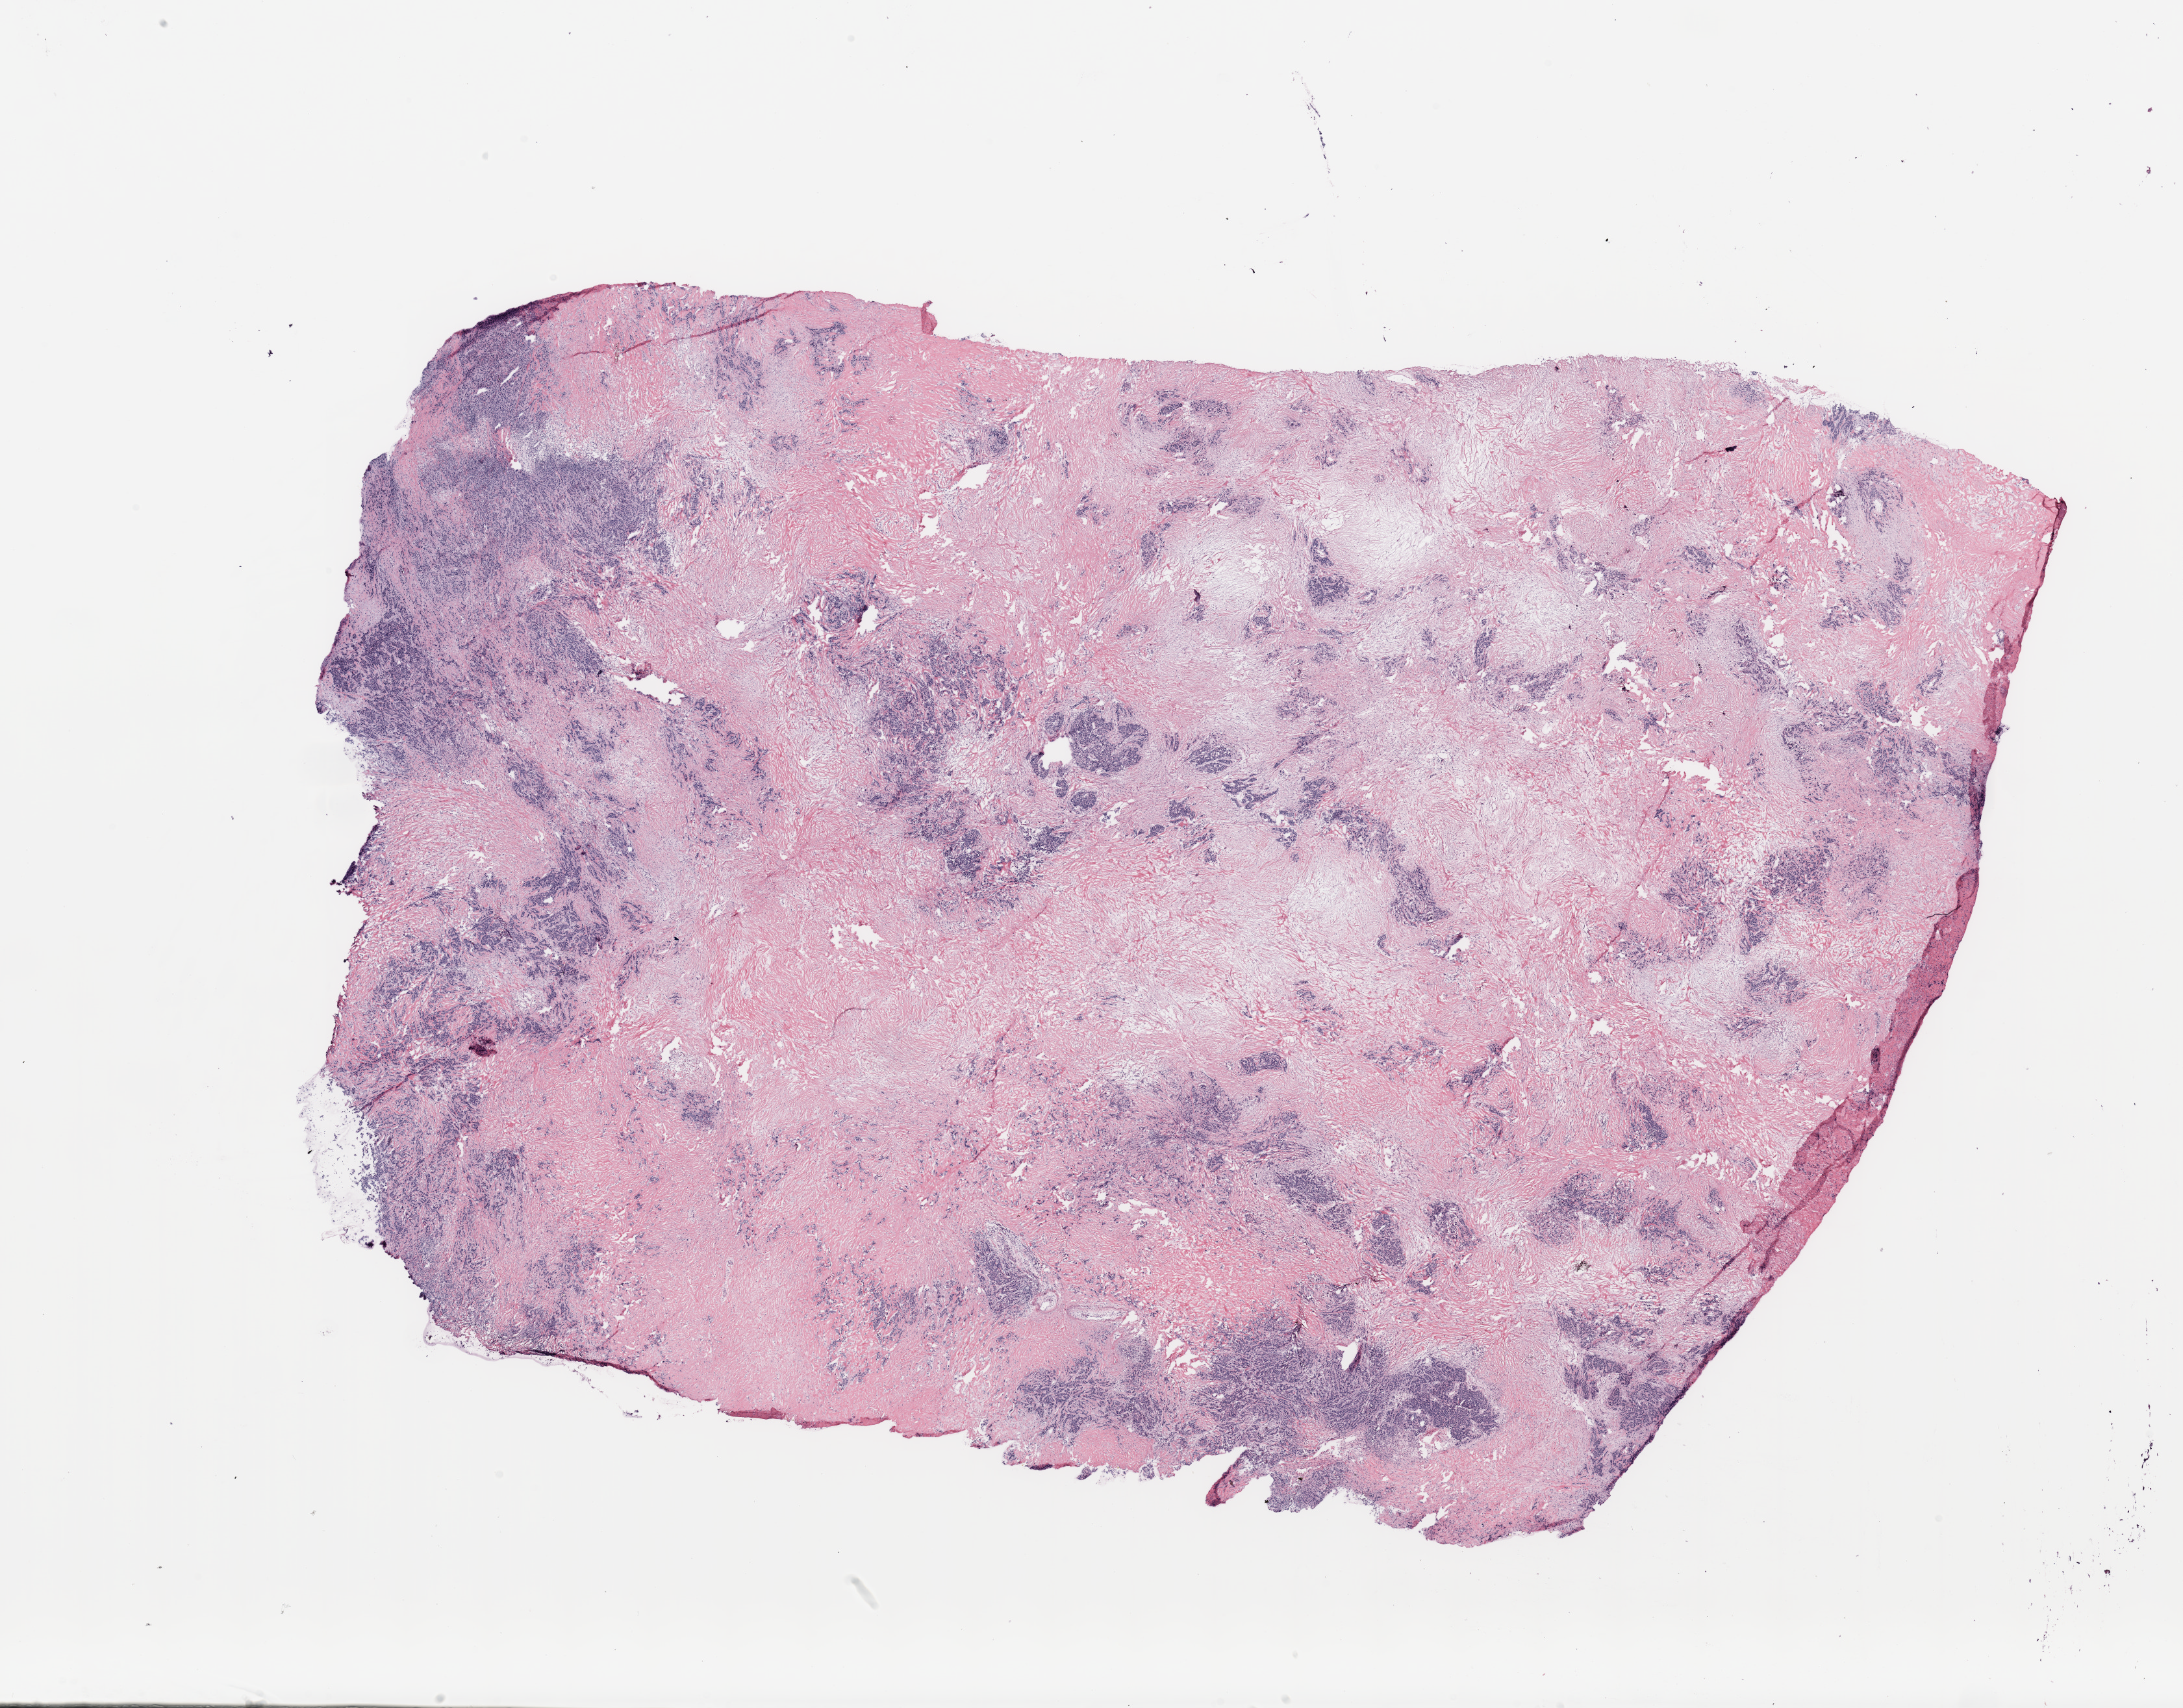
Whole-slide histology image, H&E — low-resolution overview of the scanned area, about 26.6 x 20.8 mm (from a 20x scan). Breast, tissue type not recorded.
Patient diagnosis (cohort enrolment): breast cancer (breast).